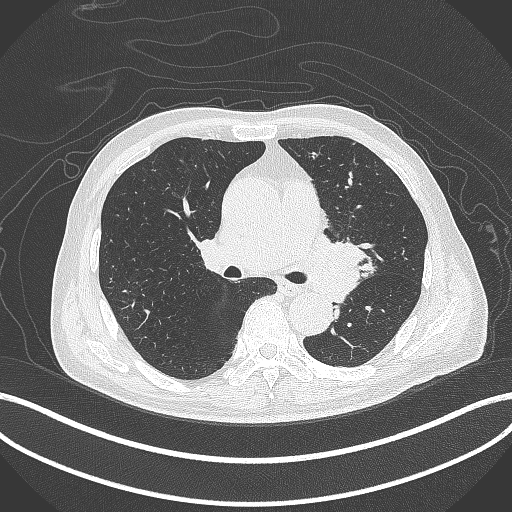
Chest CT, one axial slice; position 254 of 417 along the scan axis; reconstruction kernel B70f; 120 kVp; lung window (W 1500 / L -600 HU); 1 mm slice thickness; 512 × 512 image matrix. Male patient, age 77 years. Case-level facts recorded for this patient, not image findings: clinical TNM (as recorded): T3 N1 M0.
Annotated regions visible in this slice (rectangle marked by the reading radiologist):
- lung tumour (recorded histology: adenocarcinoma): bounding box (x1, y1, x2, y2) in pixels: (306, 231, 375, 302)